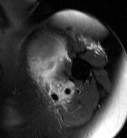
MRI of an extremity soft-tissue mass, one axial slice. Position 58 of 87 along the scan axis. T2-weighted fat-saturated. MR volume resampled by the dataset authors to the PET/CT grid (not the native acquisition matrix). 3.27 mm slice thickness. 127 × 138 image matrix, field of view 124 × 135 mm. Female patient. From the clinical record (not read from this slice): histological type: pleiomorphic leiomyosarcoma; grade: high; site of the primary tumour: left biceps.
Annotated regions visible in this slice (expert contour drawn on MRI and transferred to this co-registered scan by the dataset authors):
- gross tumour volume including surrounding oedema: bounding box [x1, y1, x2, y2] px = [27, 36, 67, 92]
- gross tumour volume (mass): [27, 36, 67, 81]